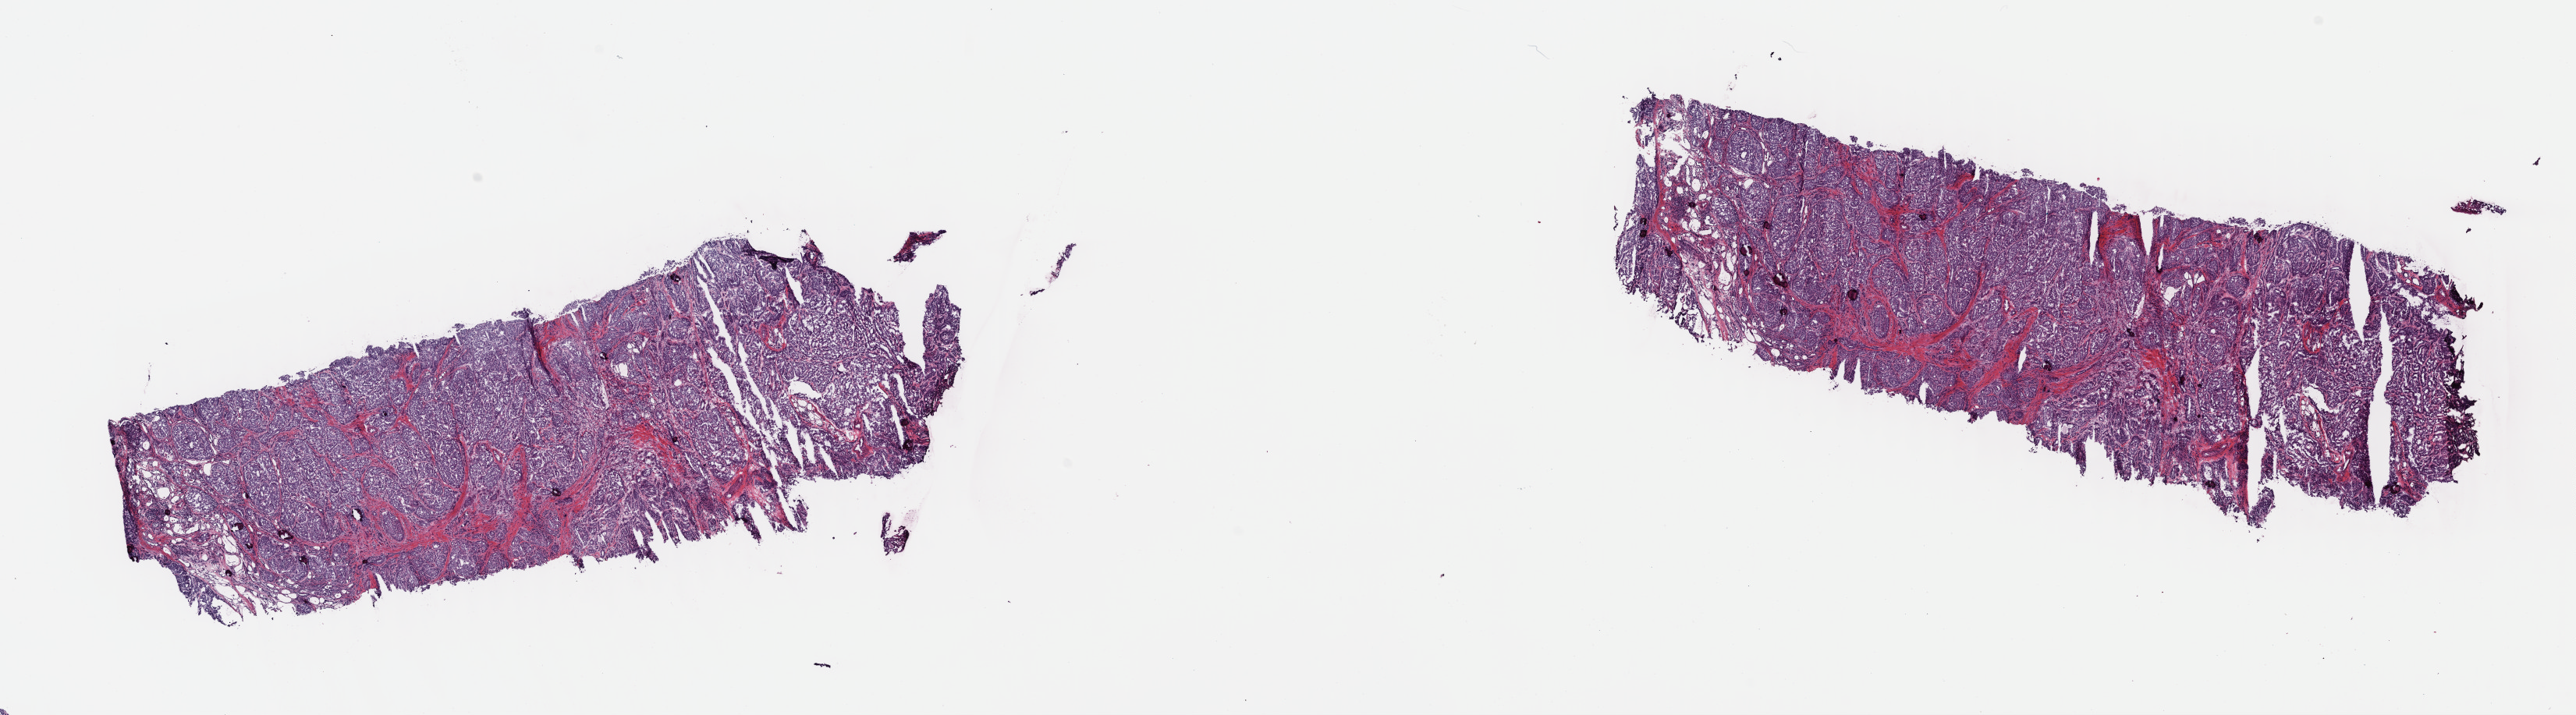
H&E whole-slide image — a low-resolution overview of the entire scanned area, about 26.0 x 7.2 mm (acquisition: 40x scan); frozen section from the top of the tissue portion; thyroid, primary tumour sample. Female patient; age at initial diagnosis 41 years. Pathologist review of this section (percent, as recorded): tumour cells 85%, tumour nuclei 100%, normal cells 0%, stromal cells 15%, necrosis 0%. Inflammatory infiltration, as recorded: lymphocyte infiltration 1%, monocyte infiltration 1%, neutrophil infiltration 0%.
AJCC pathologic stage: I (7th edition). Pathologic diagnosis: Papillary adenocarcinoma, NOS (thyroid gland). Laterality: left.